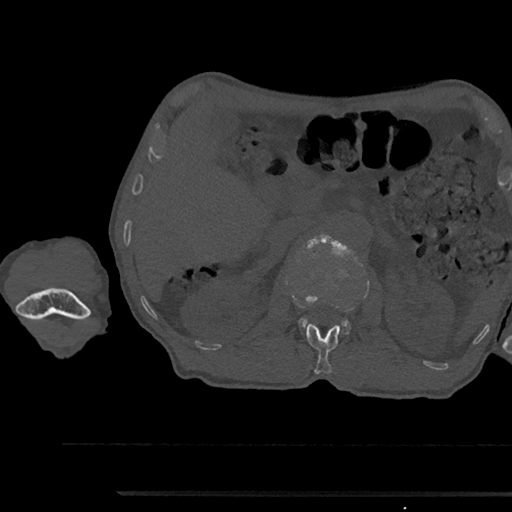
CT including the spine, one axial slice; slice 610 of 797 in the series (ordered by position); reconstruction kernel Br40s/3; 120 kVp; bone window (W 1800 / L 400 HU); 512 × 512 image matrix, field of view 367 × 367 mm. Male patient, age 79 years. From the clinical record (not read from this slice): primary cancer: prostate.
Outlined on this slice (semi-automatic segmentation, software-assisted and operator-edited):
- L1 vertebra: bounding box <306,323,340,374> (left, top, right, bottom; pixels)
- L2 vertebra: <298,234,355,335>